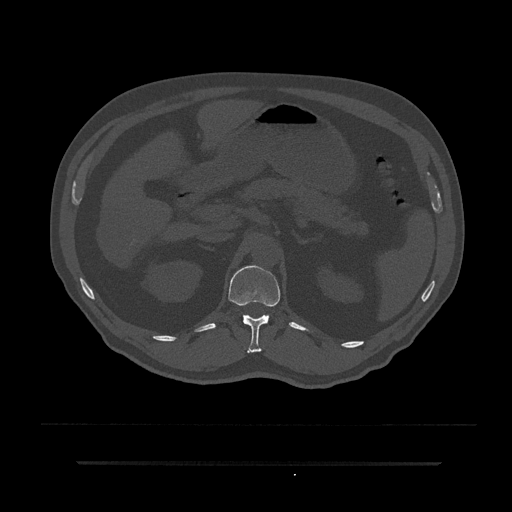
CT including the spine, one axial slice; reconstruction kernel Br40s/3; bone window (W 1800 / L 400 HU); 512 × 512 image matrix, field of view 464 × 464 mm. Male patient, age 59 years. Case-level facts recorded for this patient, not image findings: primary cancer: bile ducts; vertebrae with lytic lesions (as recorded): T10.
Outlined on this slice (semi-automatically segmented with operator editing):
- T12 vertebra: bounding box [x1, y1, x2, y2] px = [228, 265, 280, 353]